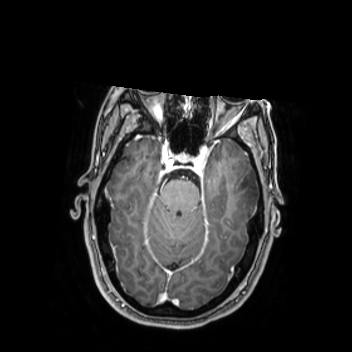
Brain MRI from a brain-tumour surgery series, one axial slice; slice 170 of 350 in the series (ordered by position); T1-weighted post-contrast; 0.9 mm slice thickness; 352 × 352 image matrix. Case-level facts recorded for this patient, not image findings: histopathology: Oligodendroglioma; WHO grade: 2; IDH mutation: yes; tumour location: Left Middle Temporal Gyrus.
Structures marked on this image (manually delineated by an expert):
- tumour: bounding box (x1, y1, x2, y2) in pixels: (228, 164, 257, 217)